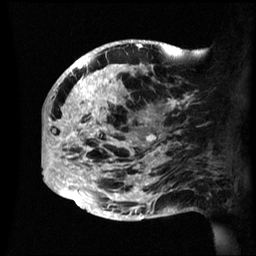
Breast MRI (dynamic contrast-enhanced), one sagittal slice; slice 23 of 60 in the series (ordered by position); dynamic contrast-enhanced series, image 2 of 3 at this slice position (ordered by acquisition); 1.5 T; TE 4.2 ms, TR 8.4 ms; 2.4 mm slice thickness; 256 × 256 image matrix, field of view 230 × 230 mm. Patient: female, 48 years.
Outlined on this slice (semi-automatically segmented with operator editing):
- analysis volume of interest (the breast-tissue region the enhancement analysis was run in; not a lesion): bounding box (x1, y1, x2, y2) in pixels: (43, 41, 195, 221)
- tumour enhancement mask (voxels above the 70 % enhancement threshold inside the analysis volume of interest): (43, 41, 180, 205)